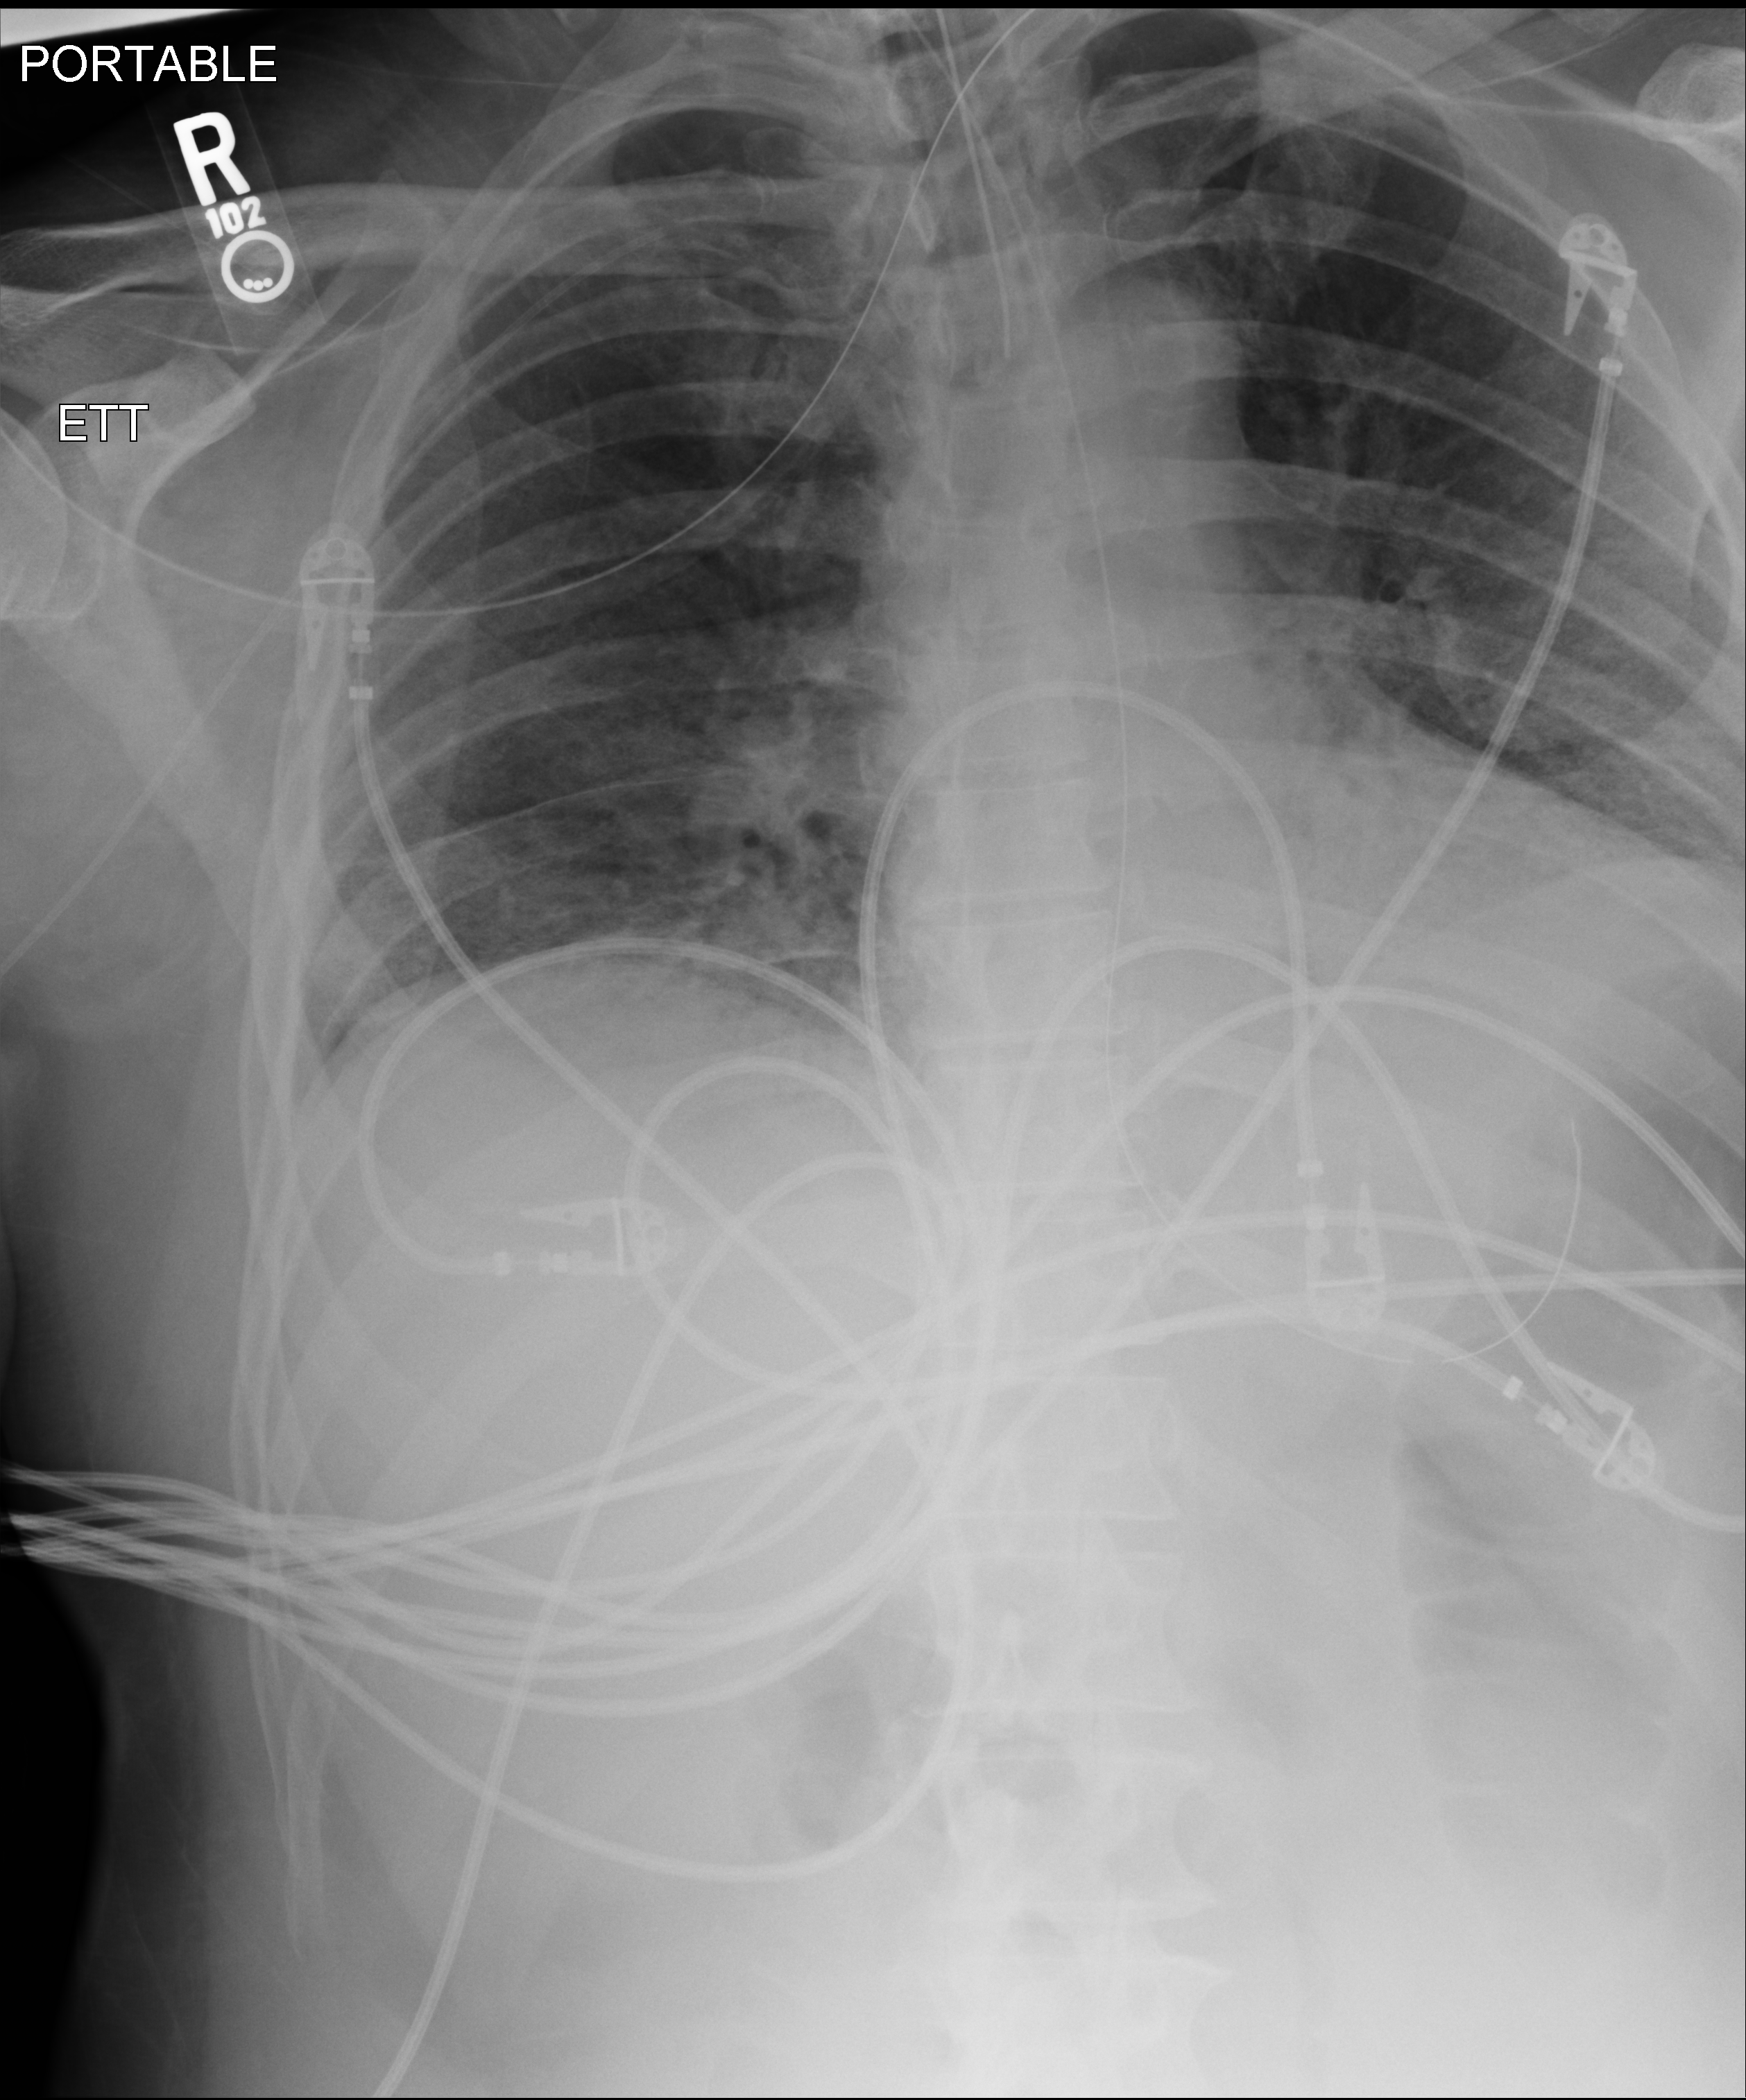
Portable chest radiograph; anteroposterior (AP) projection. Male patient hospitalised with COVID-19, age 60–74 years.
Admission-level facts for this patient (not findings on this image; timing relative to this image not recorded): length of hospital stay: 26 days; admitted to intensive care during this hospital stay: yes; mechanically ventilated during this hospital stay: yes.